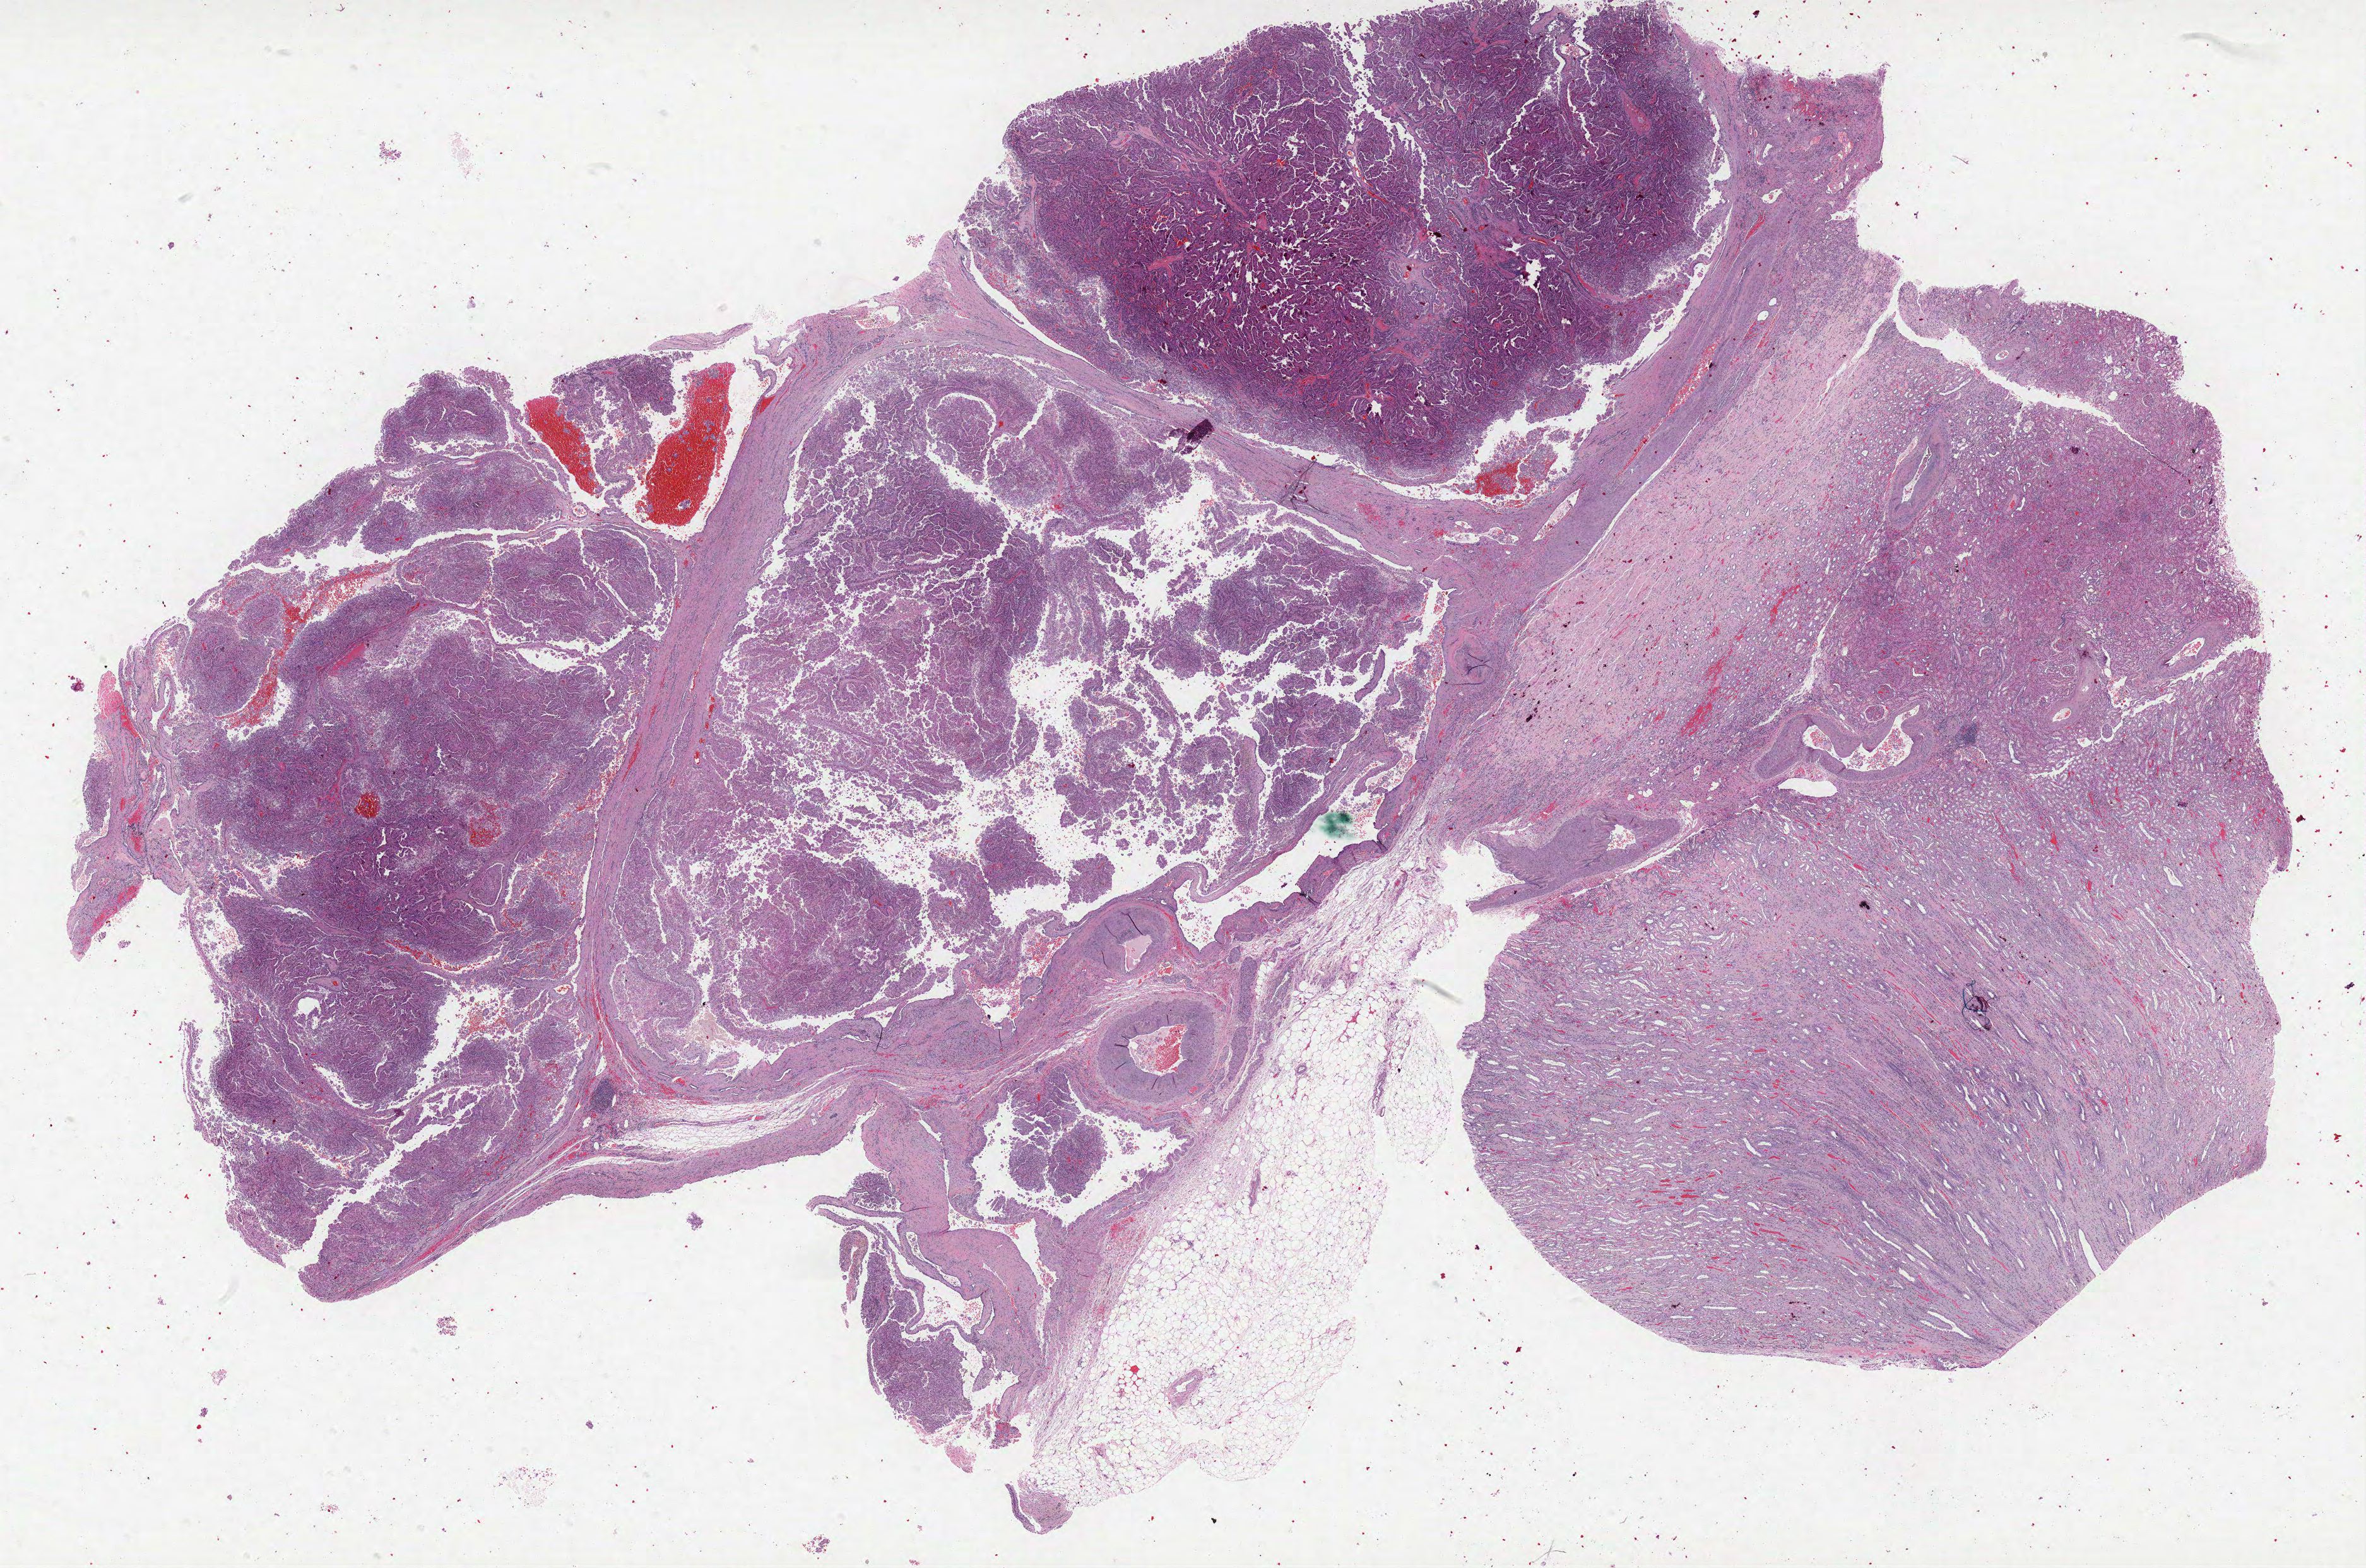
Digitized H&E-stained tissue section (whole slide) — whole scanned area (about 30.0 x 19.9 mm, acquisition: 40x scan) shown as a low-resolution overview. Formalin-fixed paraffin-embedded (FFPE) diagnostic section. Sample: primary tumour, kidney. Female patient; age at initial diagnosis 83 years.
• diagnosis: Papillary adenocarcinoma, NOS
• AJCC pathologic stage: I
• TNM: T1b NX M0